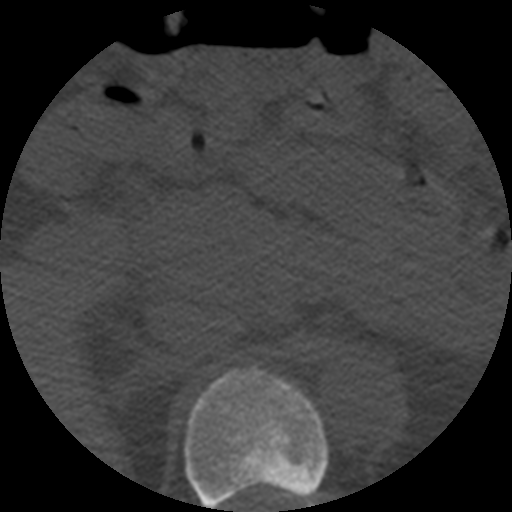
CT including the spine, one axial slice; position 235 of 508 along the scan axis; reconstruction kernel STANDARD; bone window (W 1800 / L 400 HU); 512 × 512 image matrix. Patient age 57 years. Case-level facts recorded for this patient, not image findings: primary cancer: prostate.
Structures marked on this image (semi-automatically segmented with operator editing):
- T11 vertebra: box from (x=184, y=368) to (x=329, y=512) px